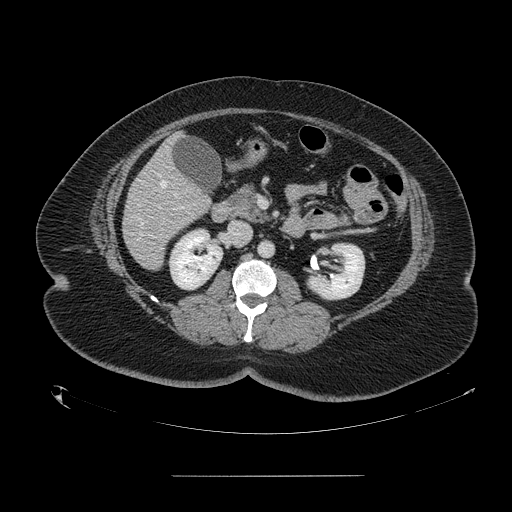
Contrast-enhanced abdominal CT, one axial slice; slice 62 of 164 in the series (ordered by position); 120 kVp; soft-tissue window (W 400 / L 40 HU); 2.5 mm slice thickness; 512 × 512 image matrix, field of view 495 × 495 mm. Female patient, age 52 years. Case-level facts recorded for this patient, not image findings: diagnosis: colorectal cancer liver metastases, imaged before liver resection; multiple liver metastases: yes.
Outlined on this slice (manually delineated by an expert):
- hepatic veins: bounding box [x1, y1, x2, y2] px = [137, 181, 175, 241]
- liver: [123, 138, 210, 269]
- portal vein (with intrahepatic branches): [173, 194, 177, 197]